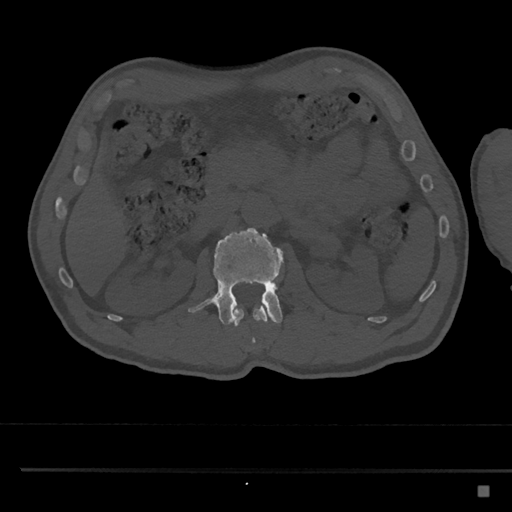
CT including the spine, one axial slice. Position 782 of 797 along the scan axis. Reconstruction kernel Br40s/3. 120 kVp. Bone window (W 1800 / L 400 HU). 0.5 mm slice thickness. 512 × 512 image matrix, field of view 391 × 391 mm. Male patient, age 59 years. From the clinical record (not read from this slice): primary cancer: prostate.
Structures marked on this image (semi-automatically segmented with operator editing):
- L1 vertebra: bounding box [x1, y1, x2, y2] px = [233, 306, 269, 343]
- L2 vertebra: [188, 228, 284, 326]